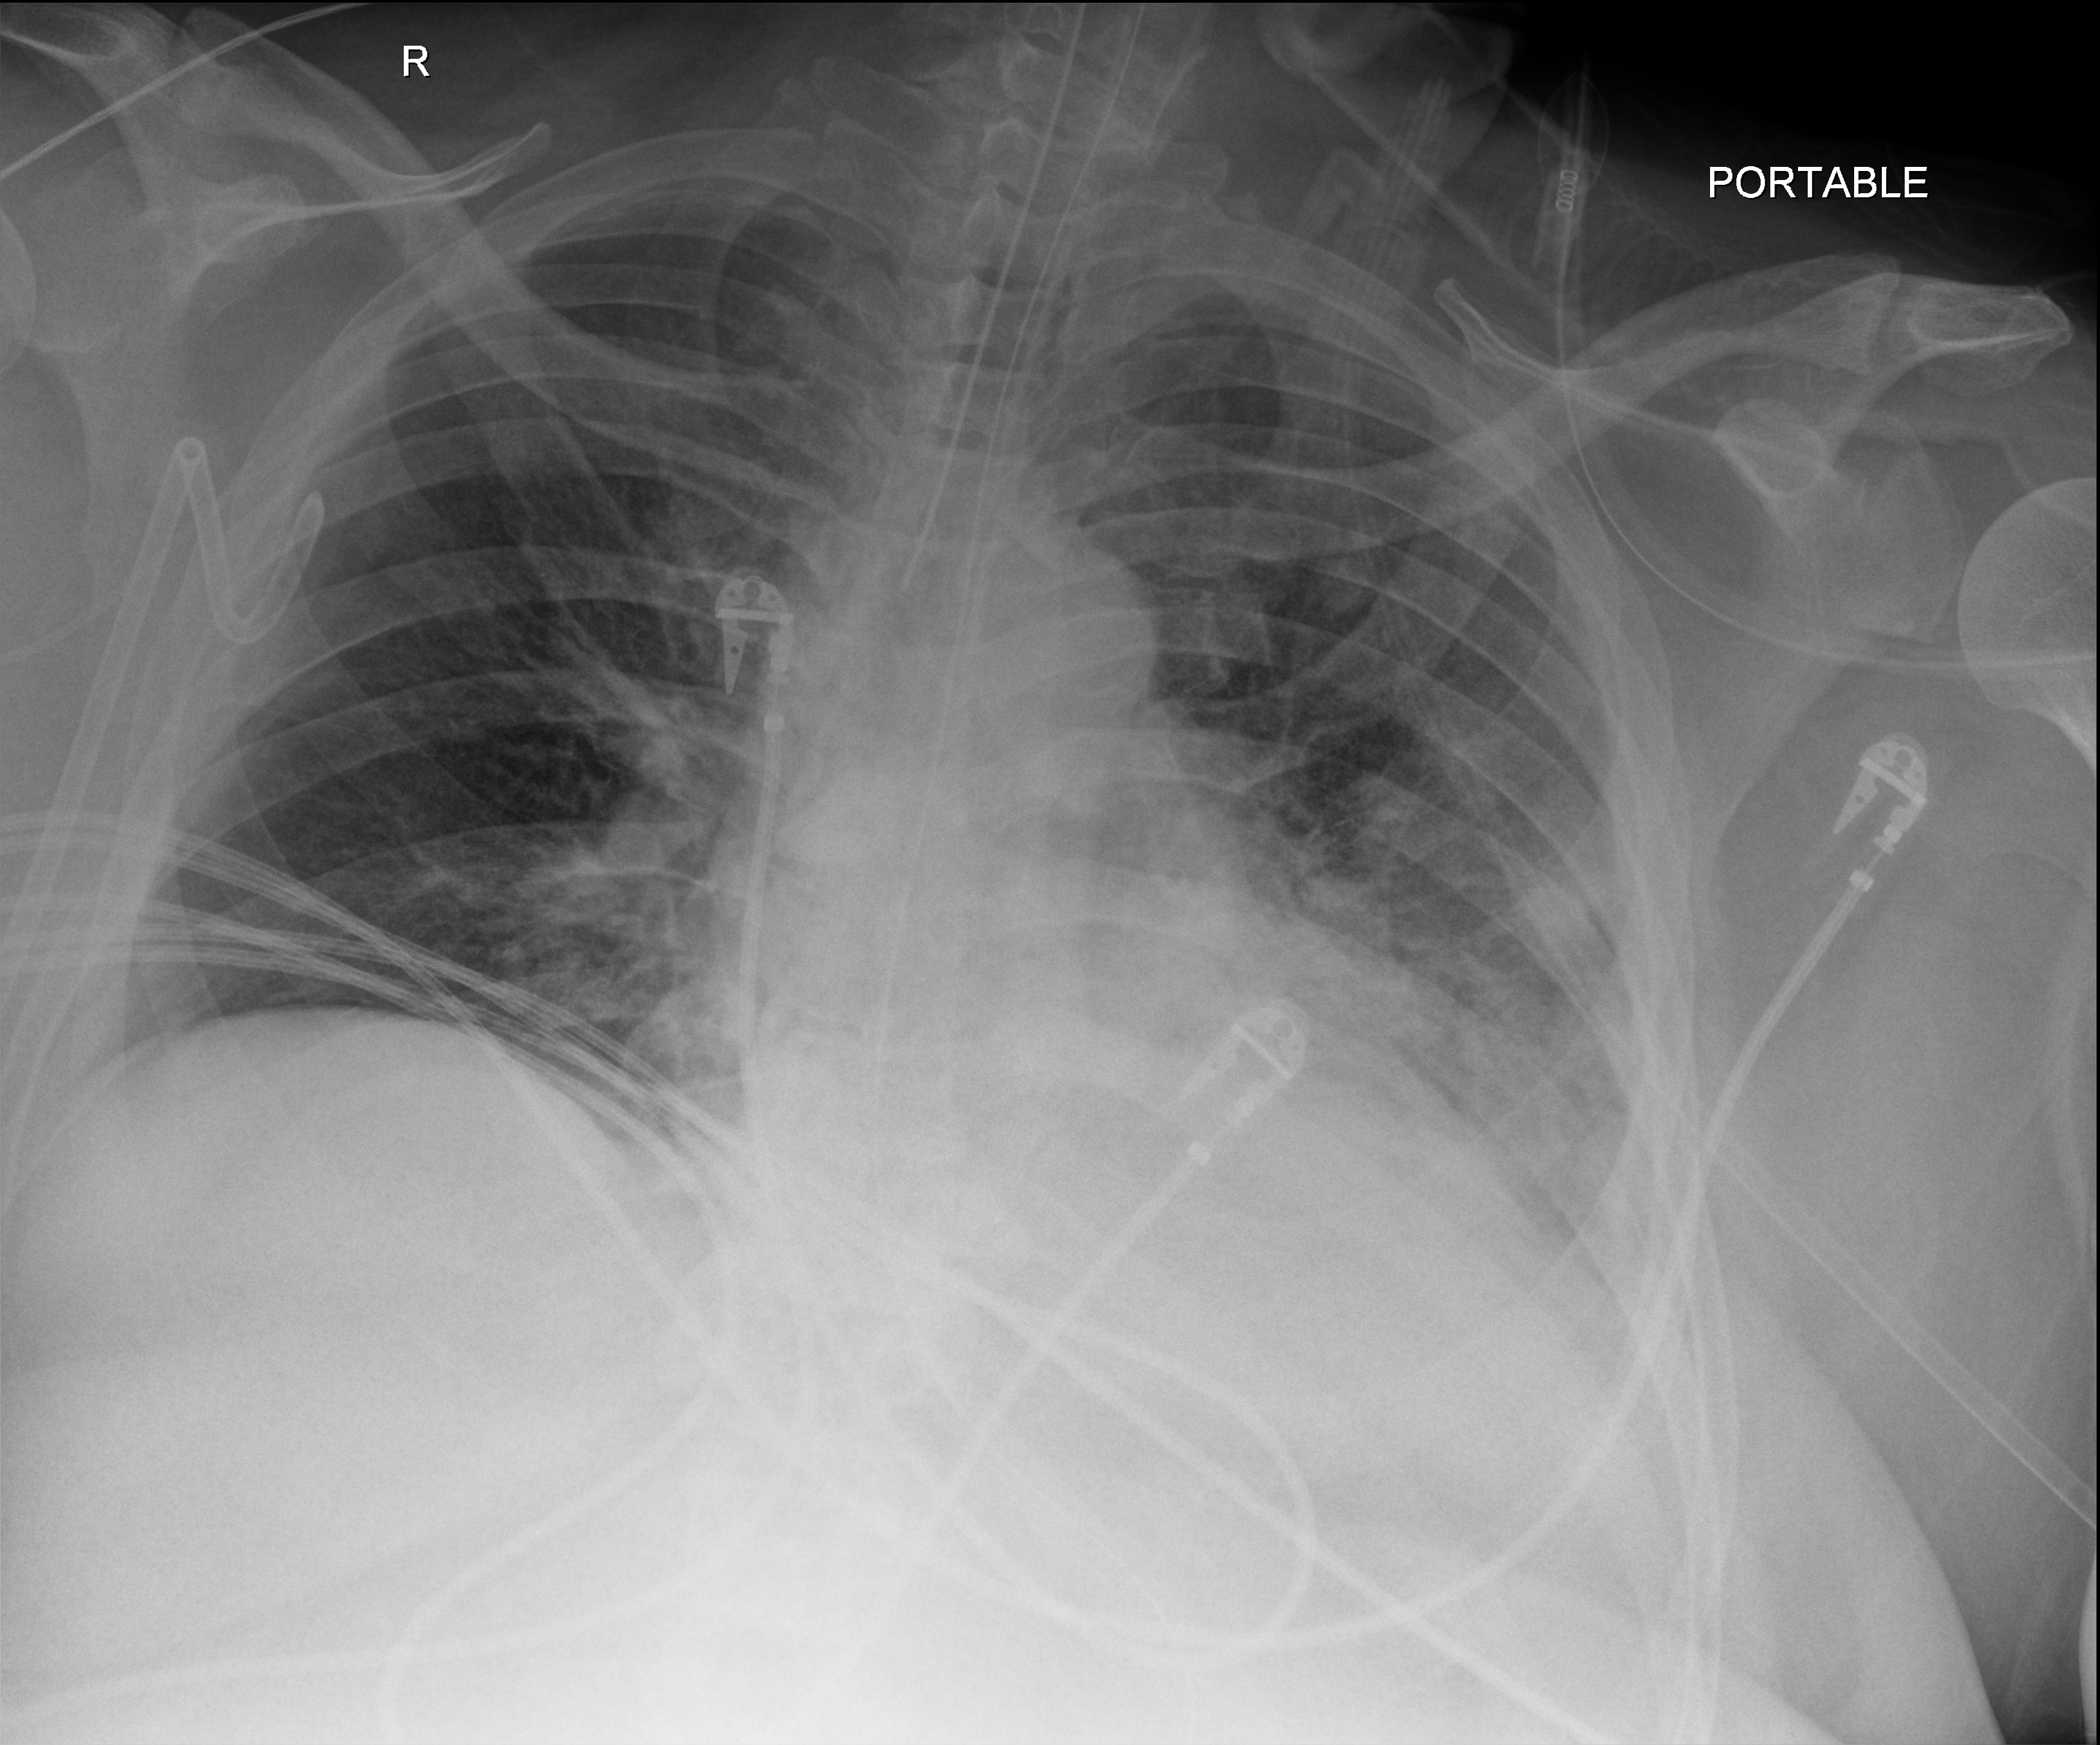
Bedside chest radiograph (digital radiography); anteroposterior (AP) projection. Male patient hospitalised with COVID-19, age 60–74 years.
Hospital-stay facts (about this admission, not read from this image; timing relative to this image not recorded): chronic kidney disease (admission record): no; diabetes (admission record): yes.